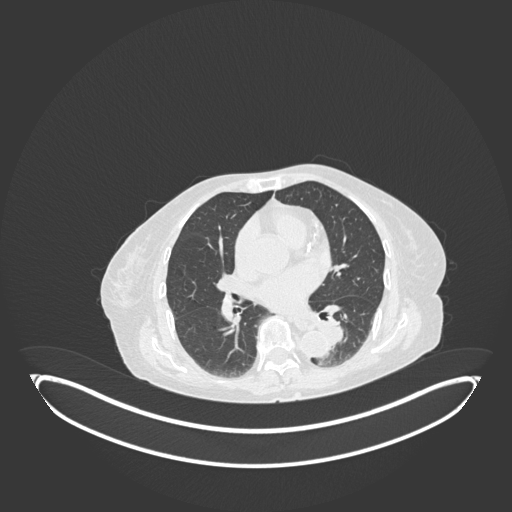
Chest CT, one axial slice. Position 58 of 189 along the scan axis. Lung window (W 1500 / L -600 HU). 512 × 512 image matrix. Patient: female, 82 years. Case-level facts recorded for this patient, not image findings: clinical TNM (as recorded): T1b N0 M1.
Structures marked on this image (bounding box drawn by a radiologist):
- lung tumour (recorded histology: adenocarcinoma): bounding box (x1, y1, x2, y2) in pixels: (315, 318, 350, 350)